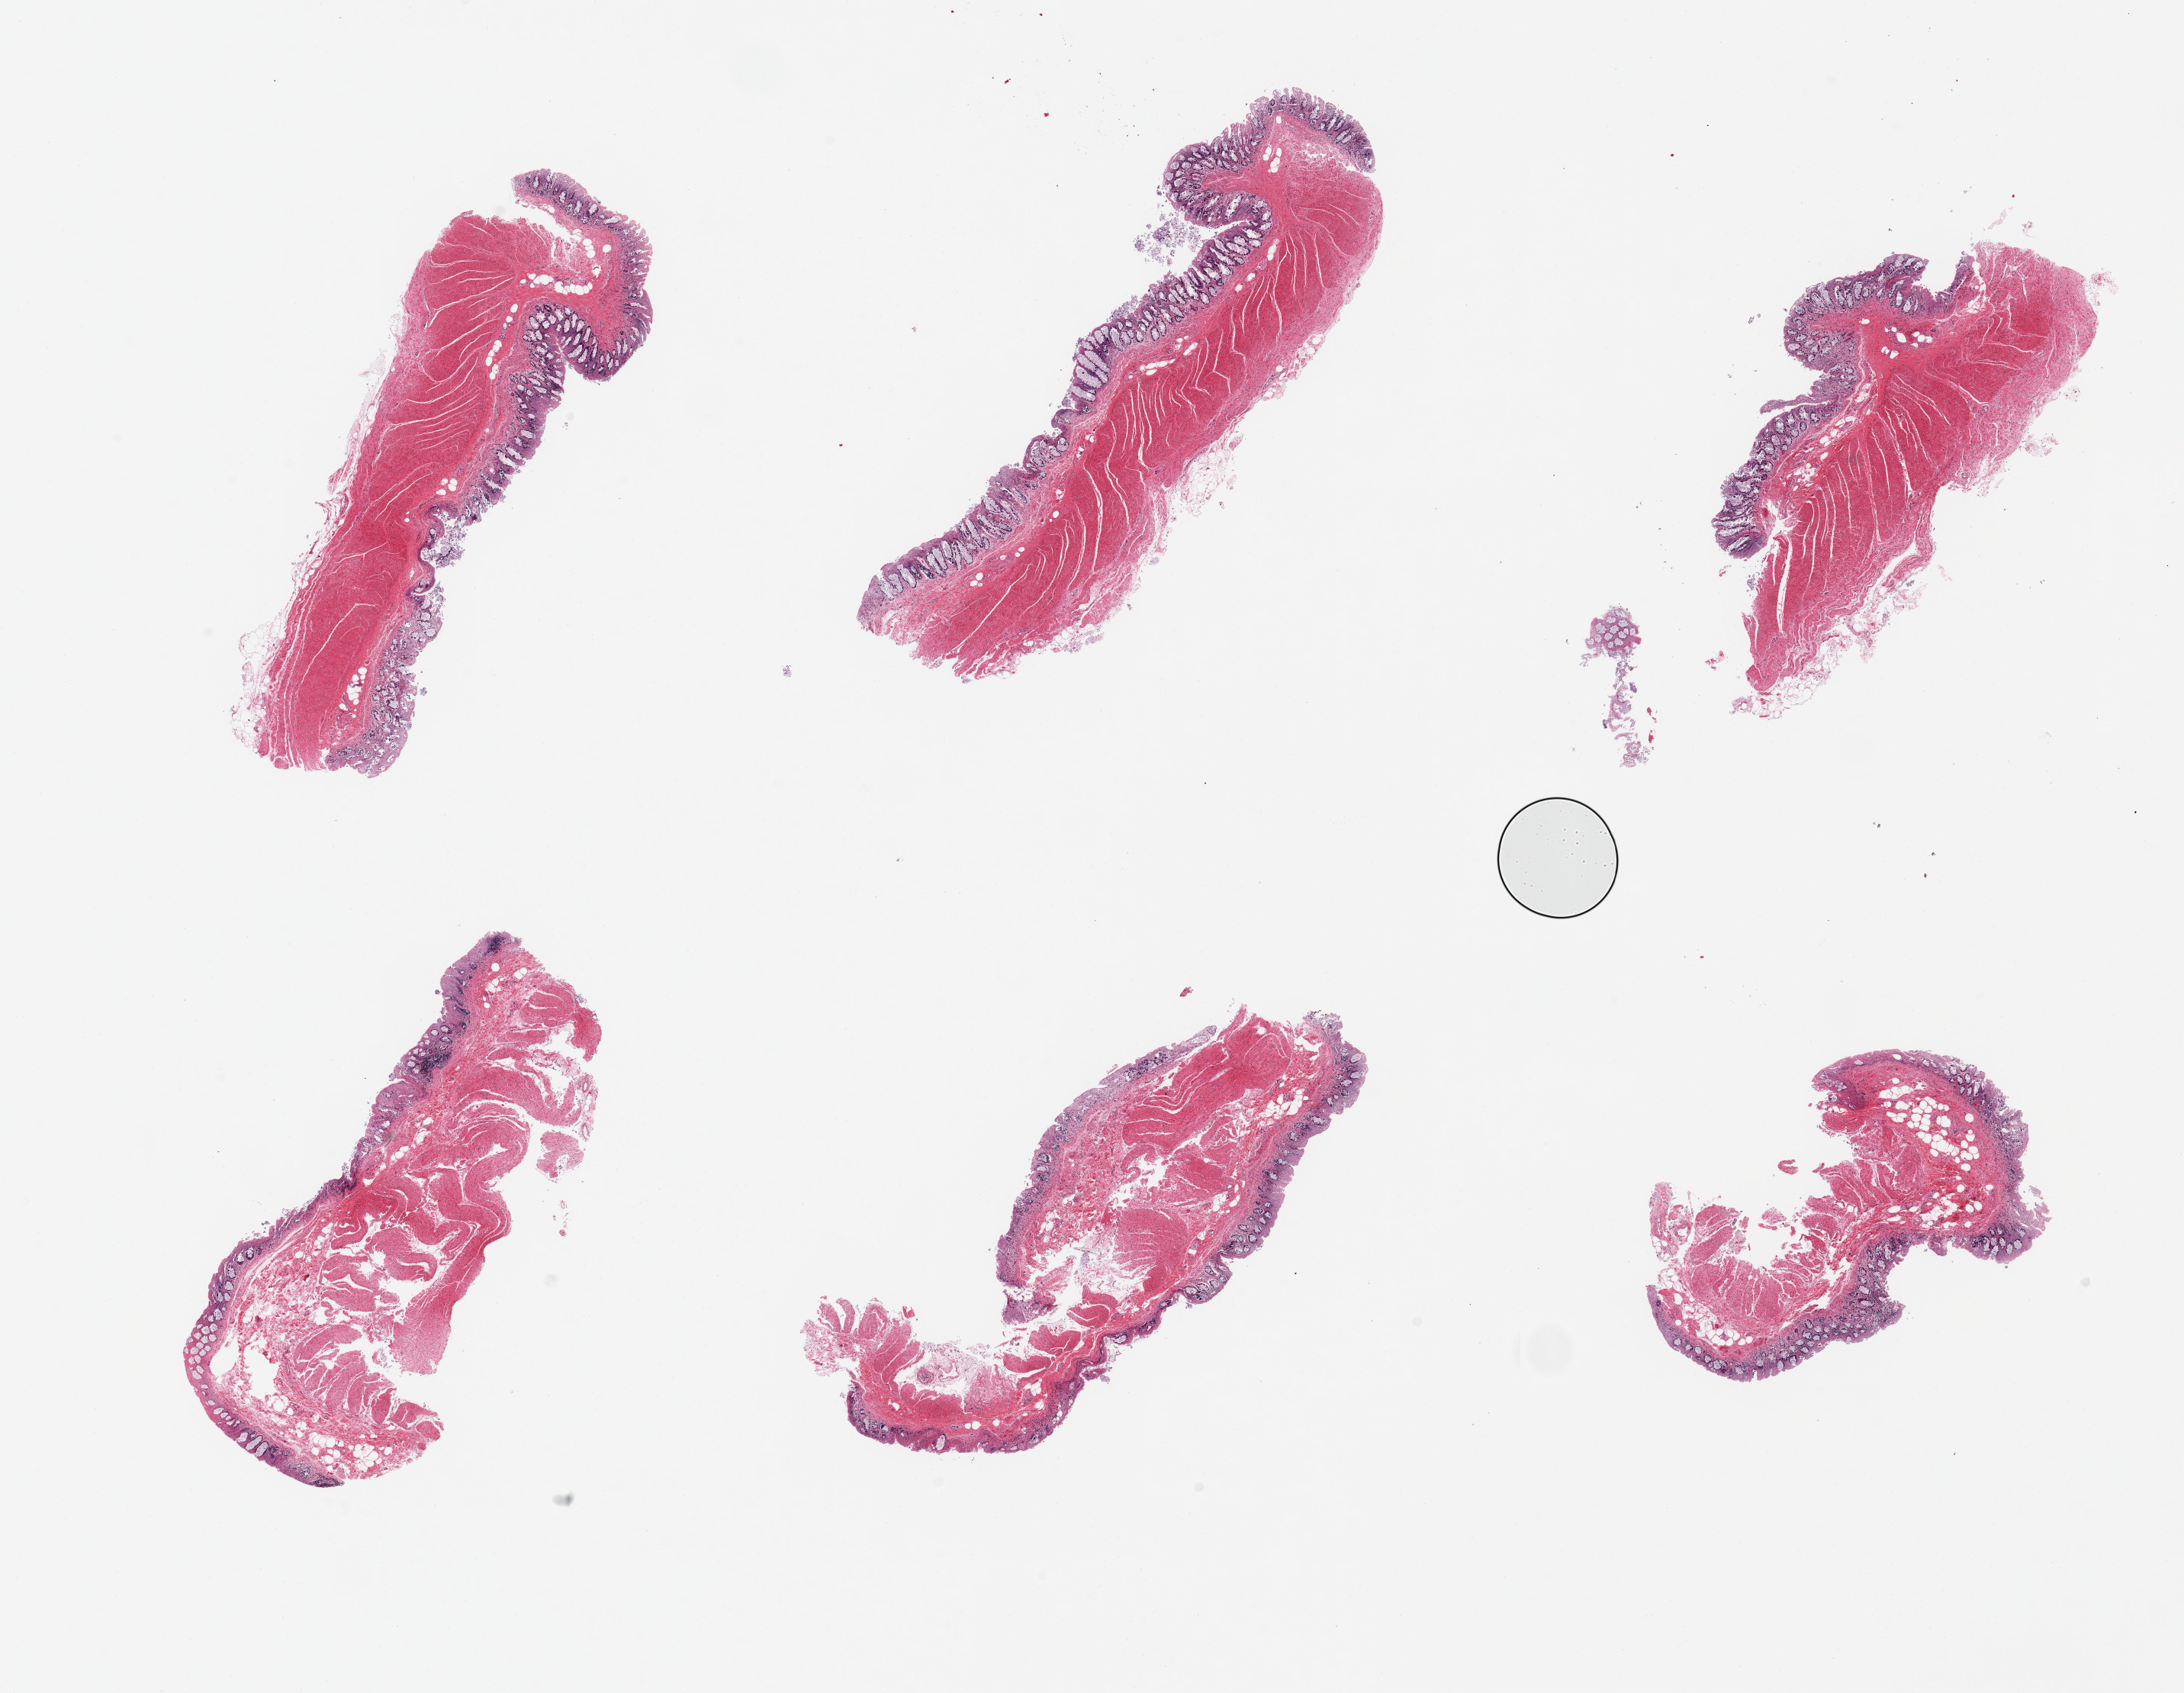
Haematoxylin and eosin whole-slide image — a low-resolution overview of the entire scanned area, about 22.6 x 17.5 mm. PAXgene-fixed, paraffin-embedded tissue. Section of sigmoid colon (target tissue). Tissue donor sample. Male donor.
* review note (as recorded): 6 pieces; full thickness sections (target is mucularis only)